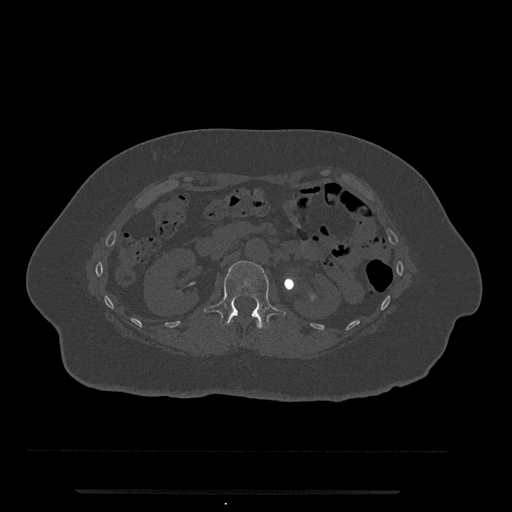
CT including the spine, one axial slice; position 113 of 797 along the scan axis; reconstruction kernel Br40s/3; 120 kVp; bone window (W 1800 / L 400 HU); 0.5 mm slice thickness; 512 × 512 image matrix, field of view 440 × 440 mm. Female patient, age 51 years. From the clinical record (not read from this slice): primary cancer: neuro; vertebrae with lytic lesions (as recorded): T8.
Structures marked on this image (semi-automatic segmentation, software-assisted and operator-edited):
- L1 vertebra: bounding box (x1, y1, x2, y2) in pixels: (203, 261, 286, 329)
- T12 vertebra: (231, 320, 261, 329)